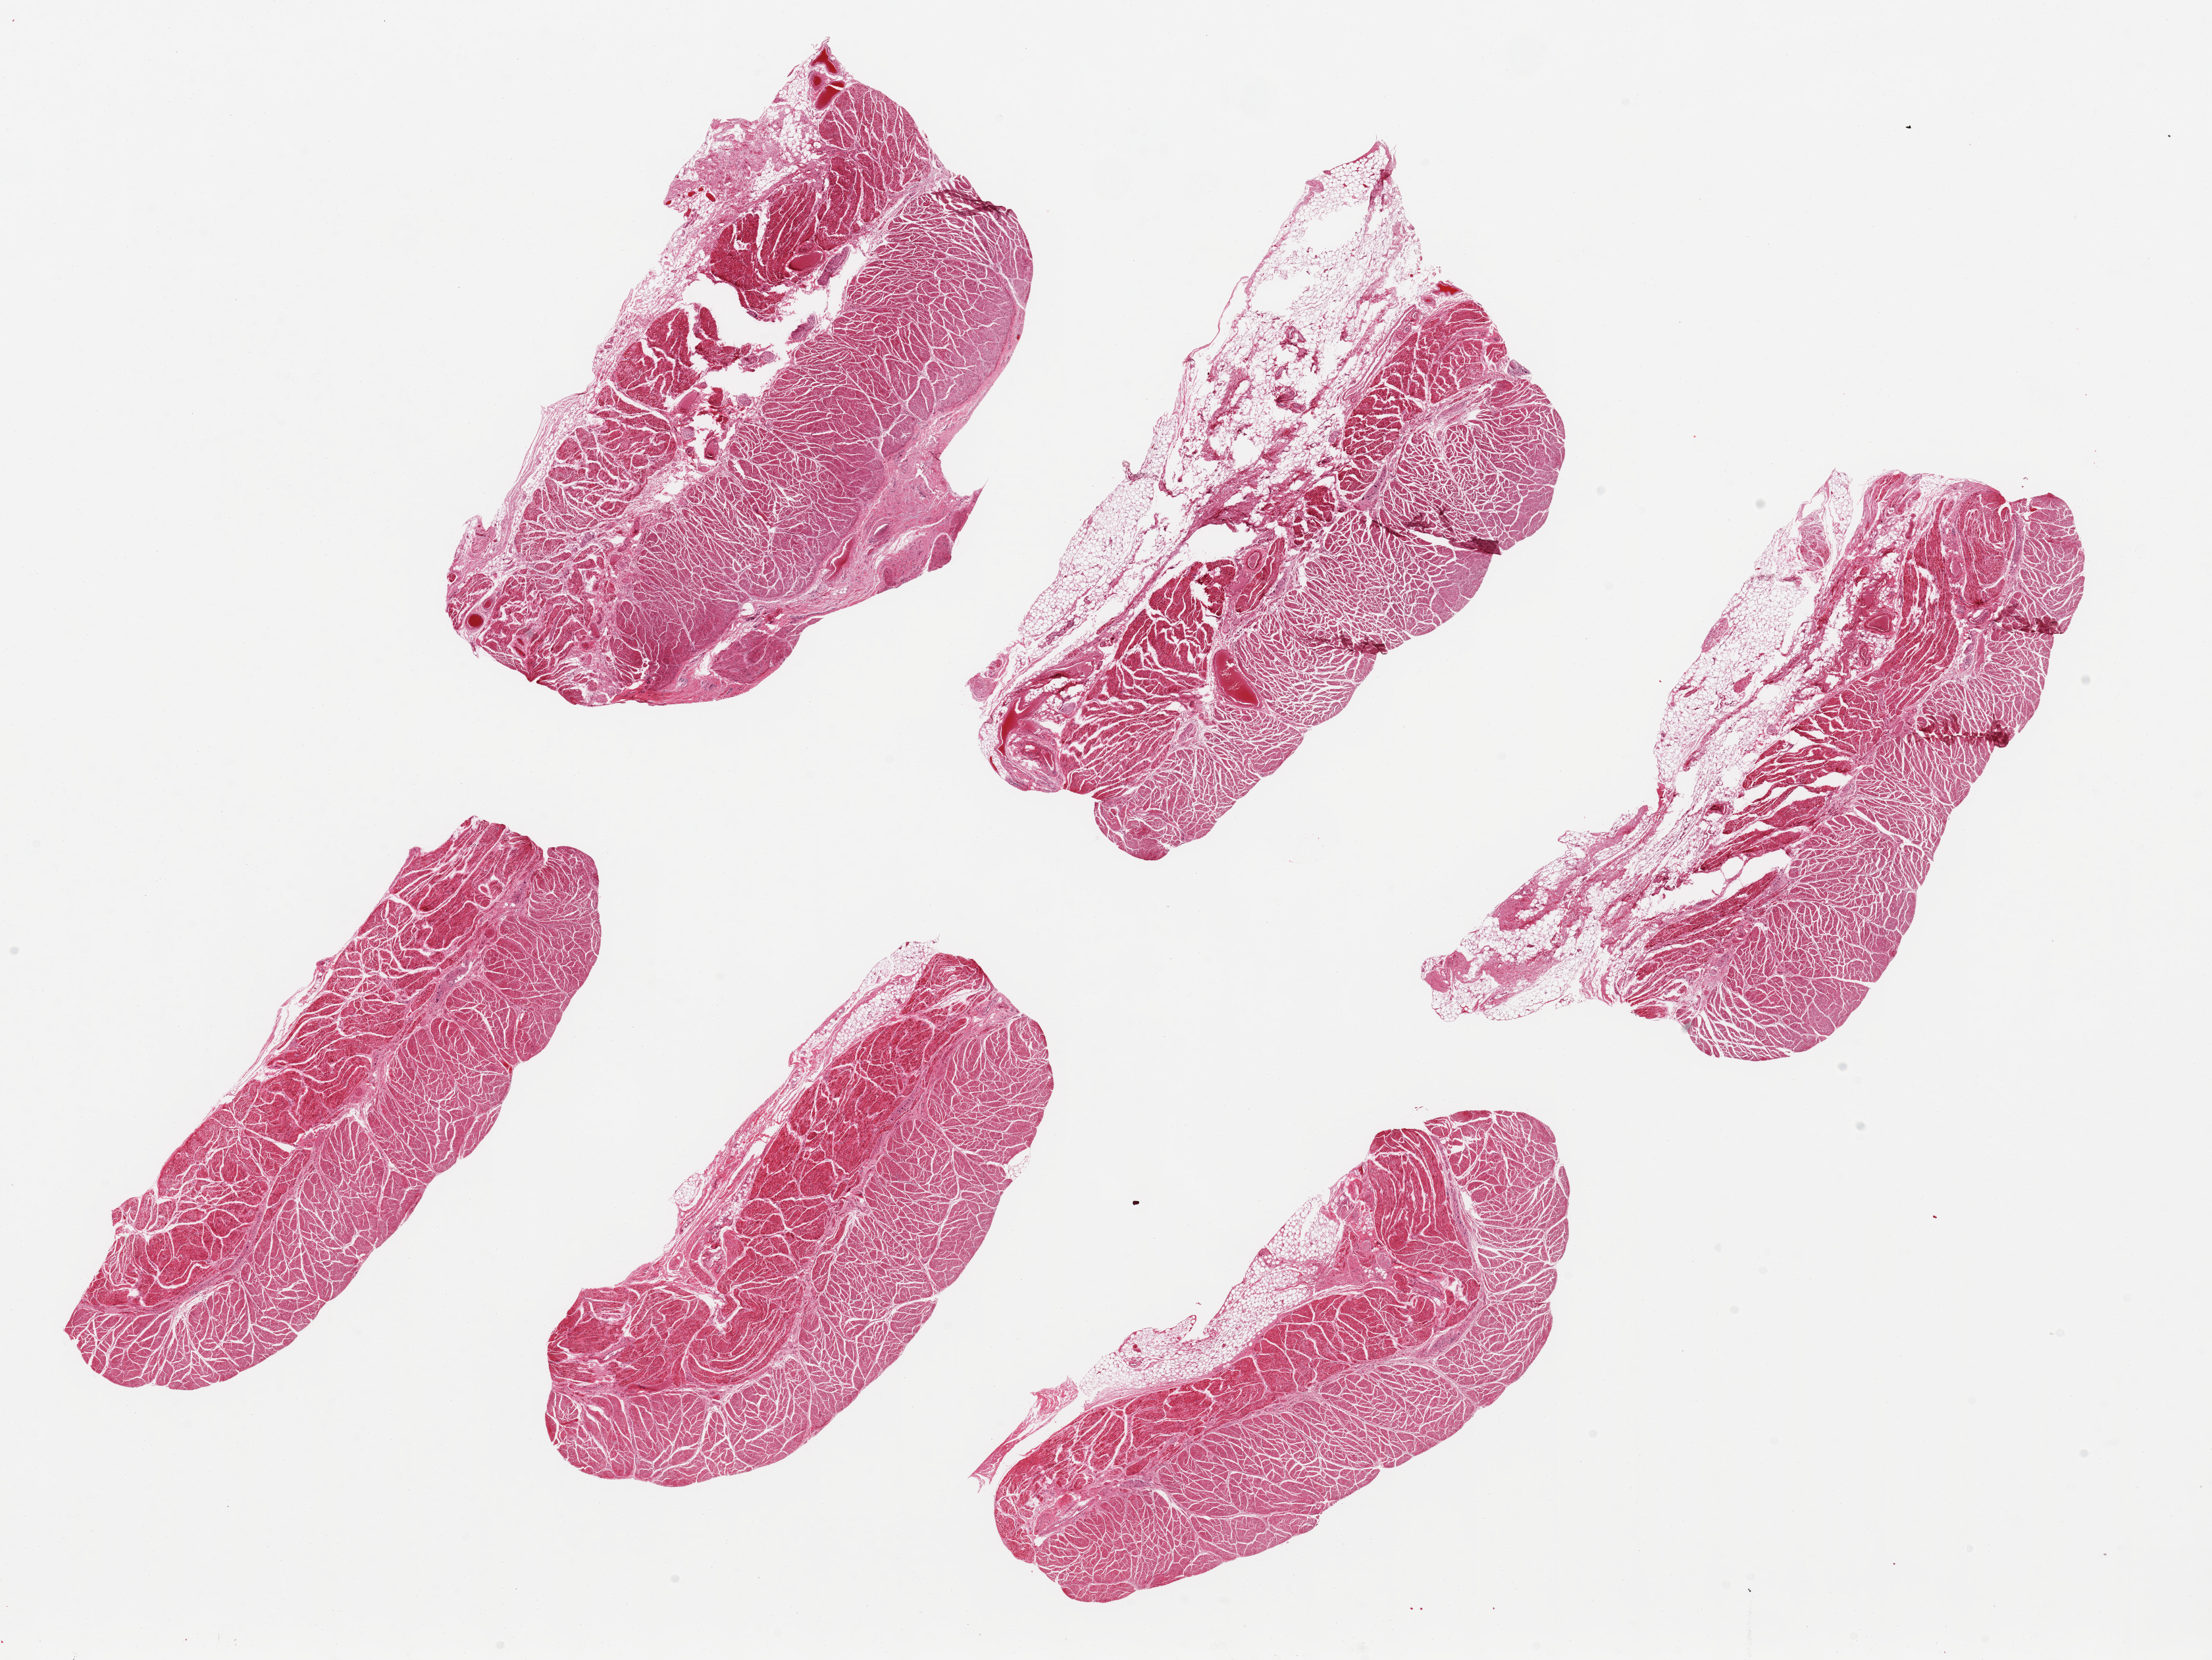
Hematoxylin and eosin (H&E) whole-slide image, a low-resolution overview of the entire scanned area, about 26.6 x 19.9 mm; PAXgene-fixed paraffin-embedded (PFPE) section; section of esophageal muscle (target tissue); tissue donor sample. Donor: male.
Pathologist's review note for this sample: 6 pieces up to 8x4 mm.